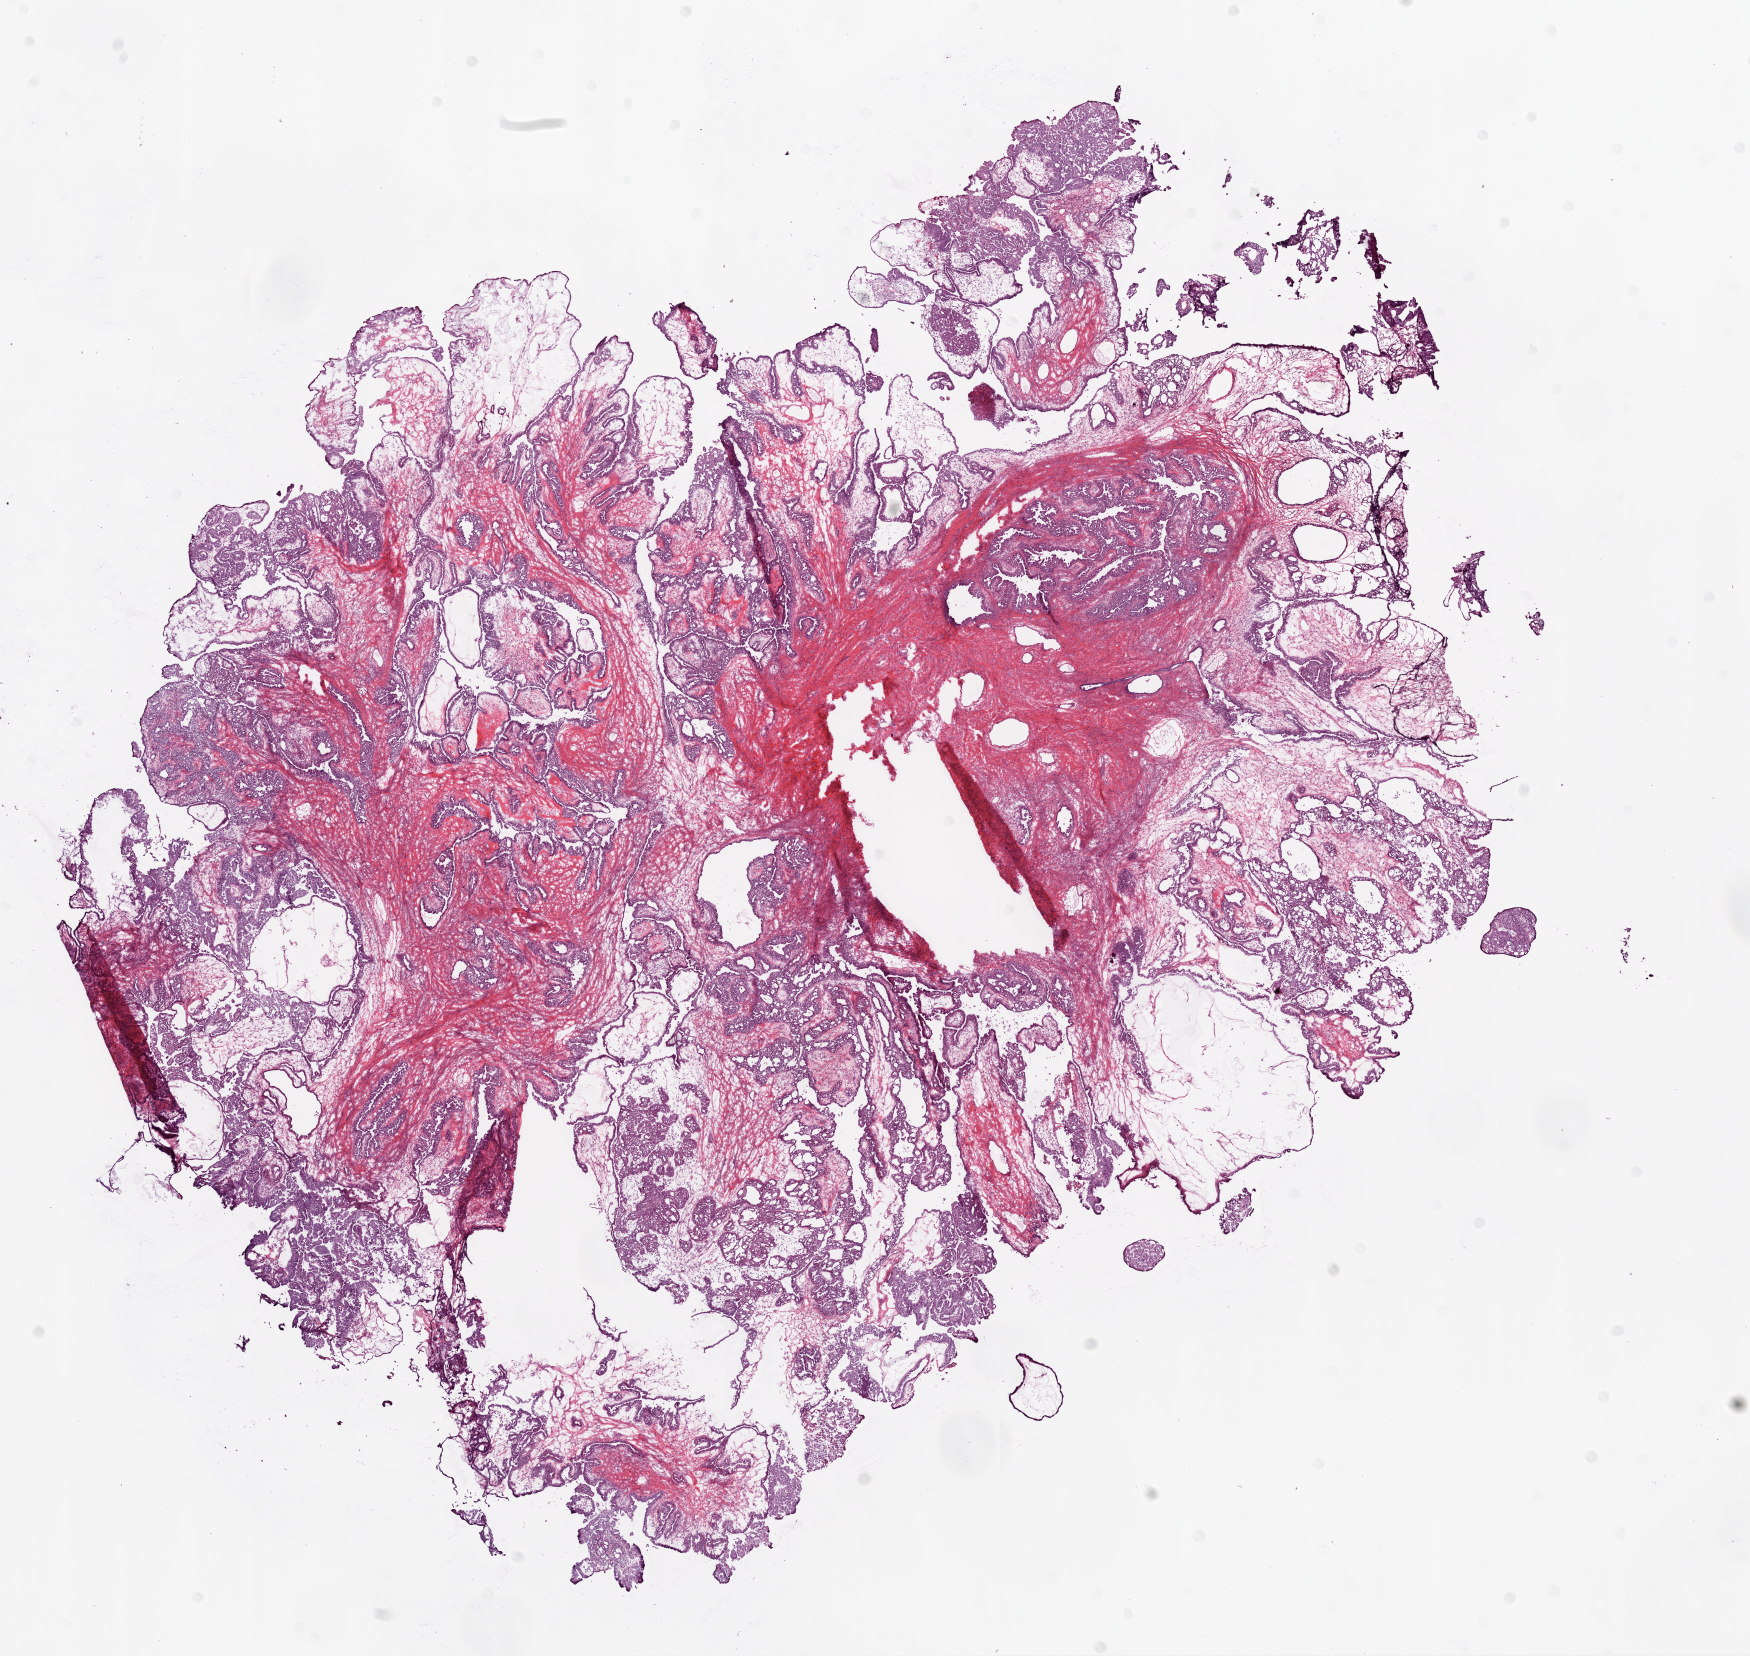
Digitized Hematoxylin and eosin (H&E) stained tissue section (whole slide), low-resolution overview of the scanned area, about 14.0 x 13.3 mm. Frozen section from the bottom of the tissue portion. Primary tumour sample from the ovary. Female patient; age at initial diagnosis 76 years. Histologic grade: G2 (moderately differentiated). Pathologist review of this section (percent, as recorded): tumour cells 40%, tumour nuclei 95%, normal cells 0%, stromal cells 60%, necrosis 0%.
FIGO stage: IIIC. Histologic diagnosis: Serous cystadenocarcinoma, NOS.